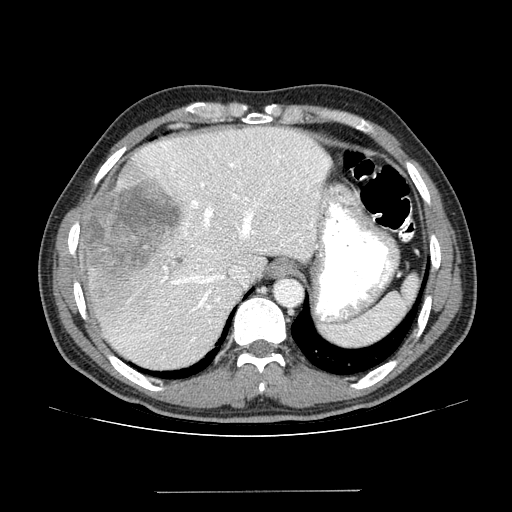
Contrast-enhanced abdominal CT (liver protocol), one axial slice. Slice 105 of 131 in the series (ordered by position). Reconstruction kernel STANDARD. 100 kVp. One of 2 acquisitions stored at this slice position. Soft-tissue window (W 400 / L 40 HU). 512 × 512 image matrix, field of view 380 × 380 mm. From the clinical record (not read from this slice): diagnosis: hepatocellular carcinoma (patient treated with transarterial chemoembolisation; whether this scan precedes or follows treatment is not stated here); TNM stage (as recorded): Stage-I; Child-Pugh class: A; tumour differentiation: poorly differentiated.
Annotated regions visible in this slice (semi-automatic segmentation, software-assisted and operator-edited):
- abdominal aorta: bounding box [x1, y1, x2, y2] px = [277, 281, 302, 305]
- liver parenchyma outside the tumour (the mass and vessels are separate outlines, so this box may not span the whole liver): [78, 126, 330, 368]
- mass: [80, 179, 179, 302]
- liver vessels: [116, 131, 328, 359]